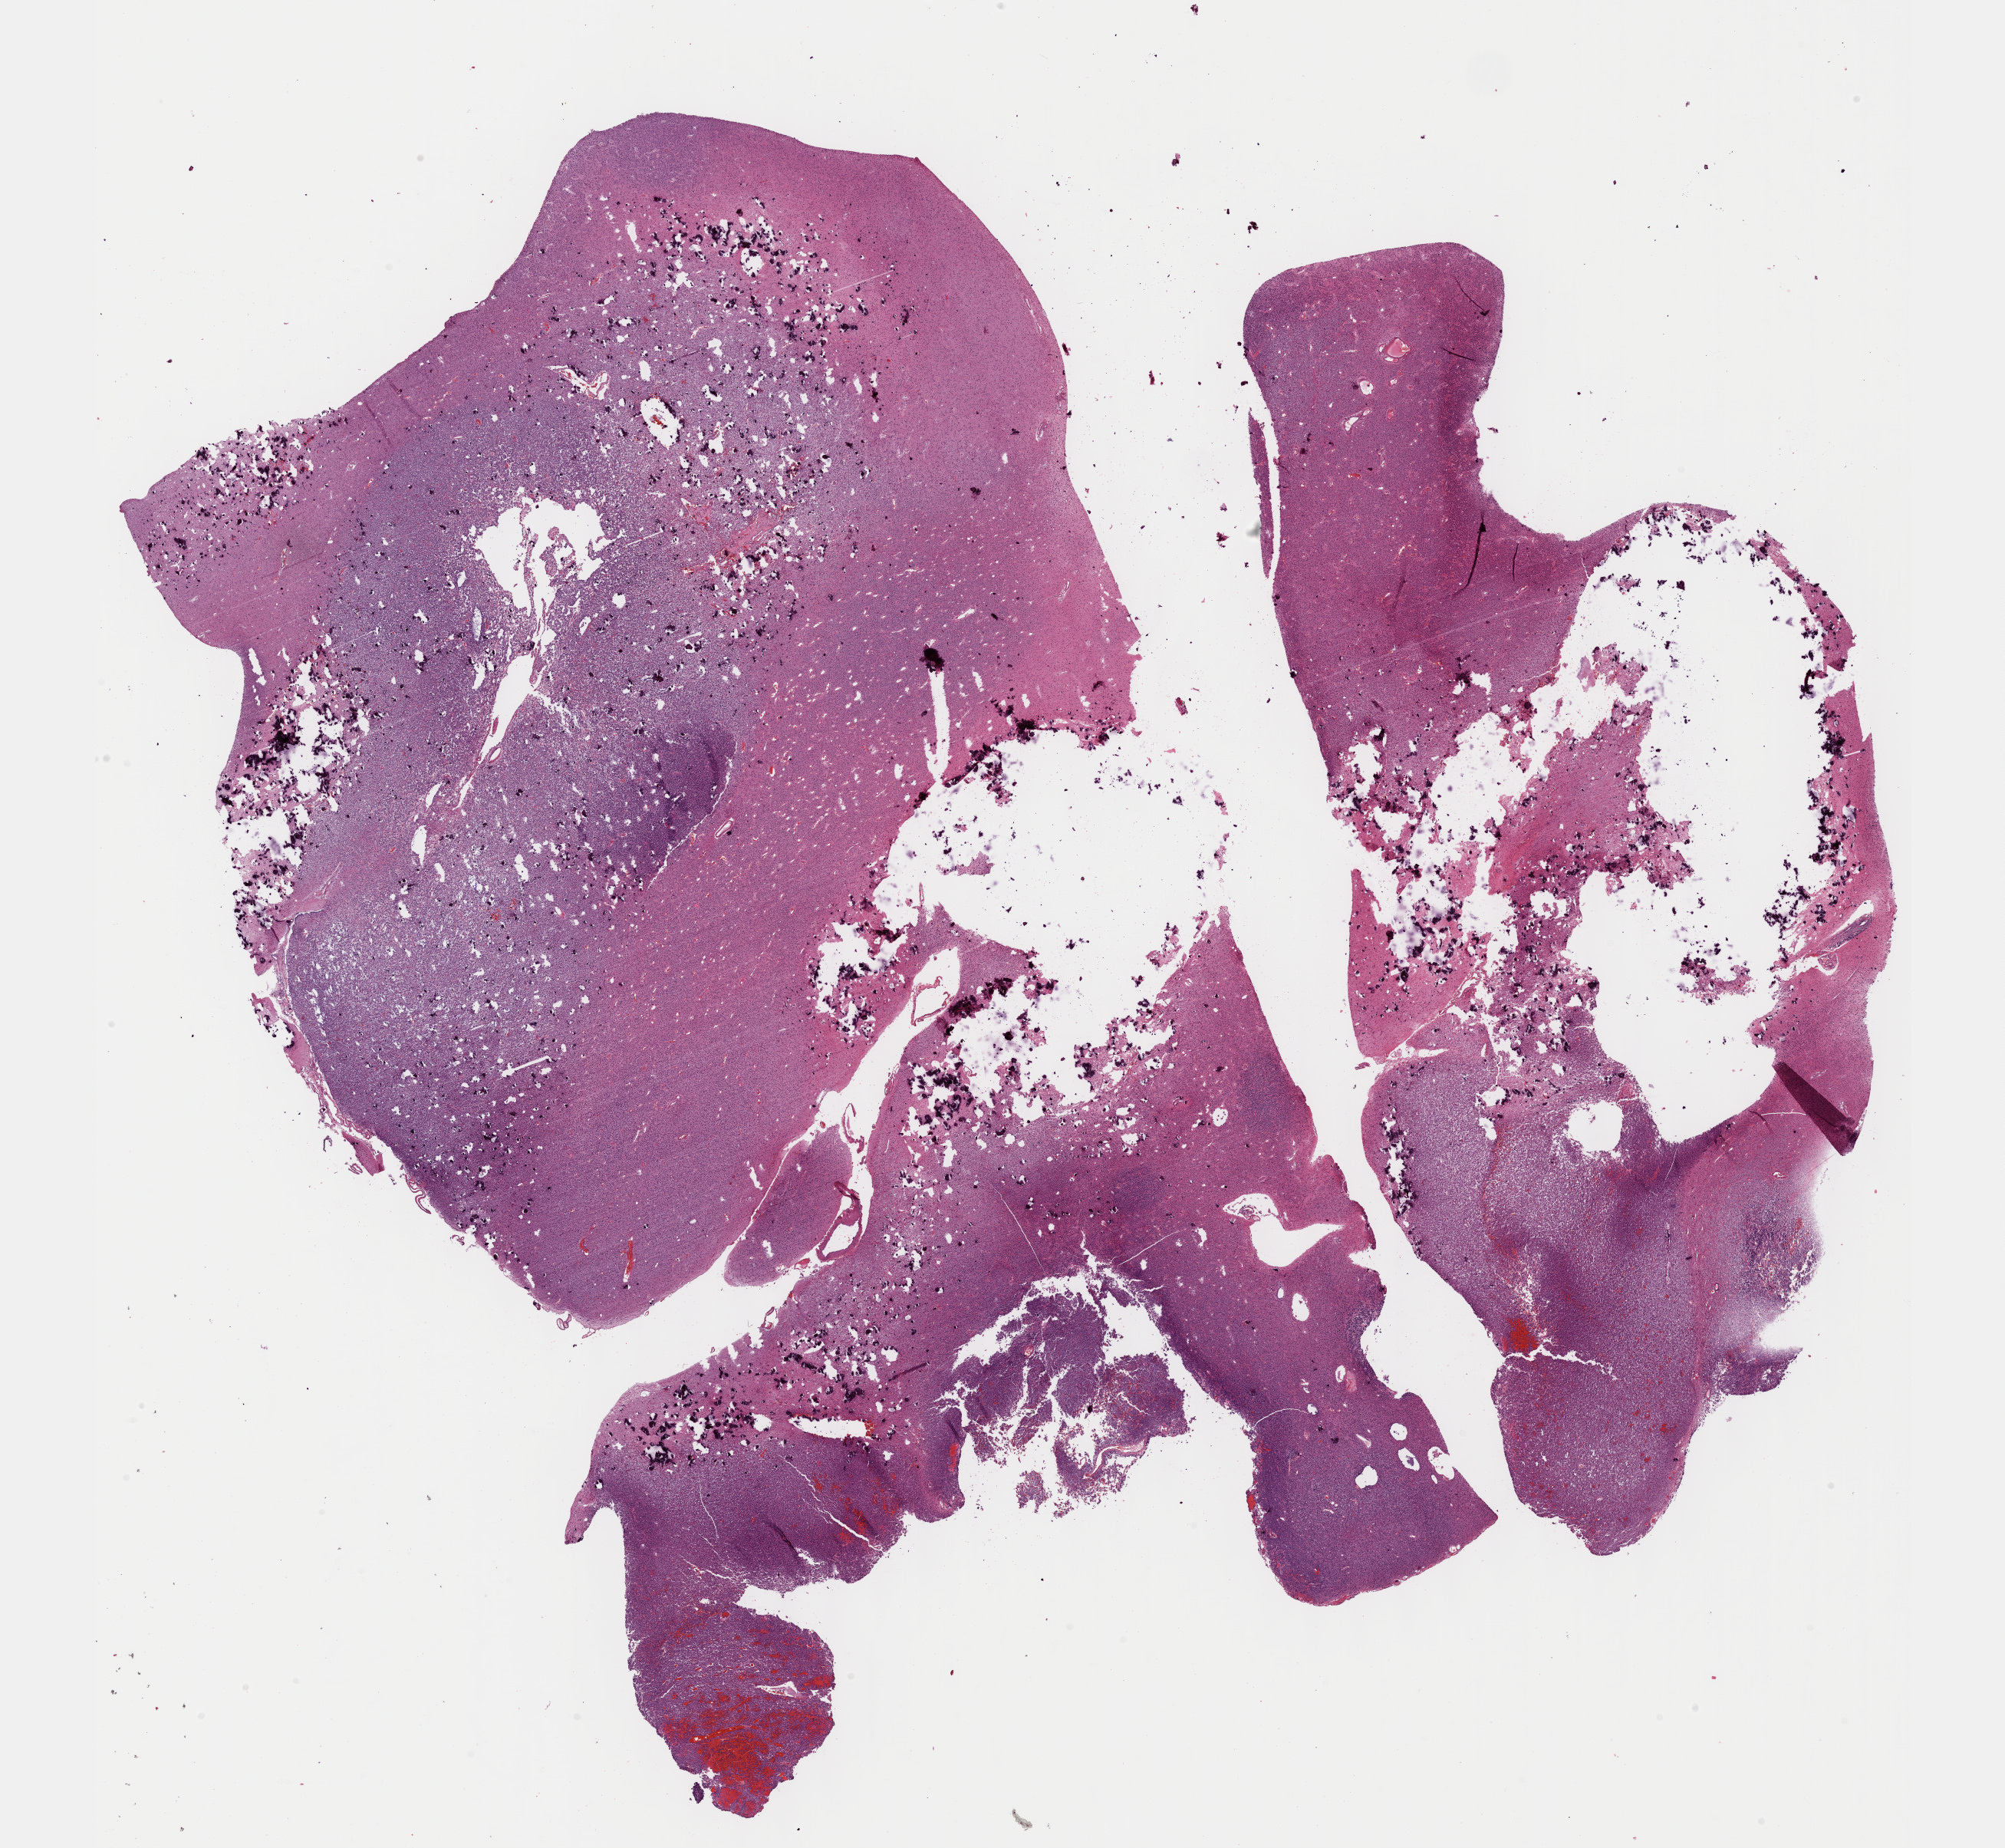
Digitized H&E tissue section (whole slide), shown as a low-resolution overview of the whole scanned area (about 21.1 x 19.5 mm). Formalin-fixed paraffin-embedded (FFPE) diagnostic section. Brain, primary tumour sample. Female patient; age at initial diagnosis 41 years.
Pathologic diagnosis: Oligodendroglioma, anaplastic (cerebrum).